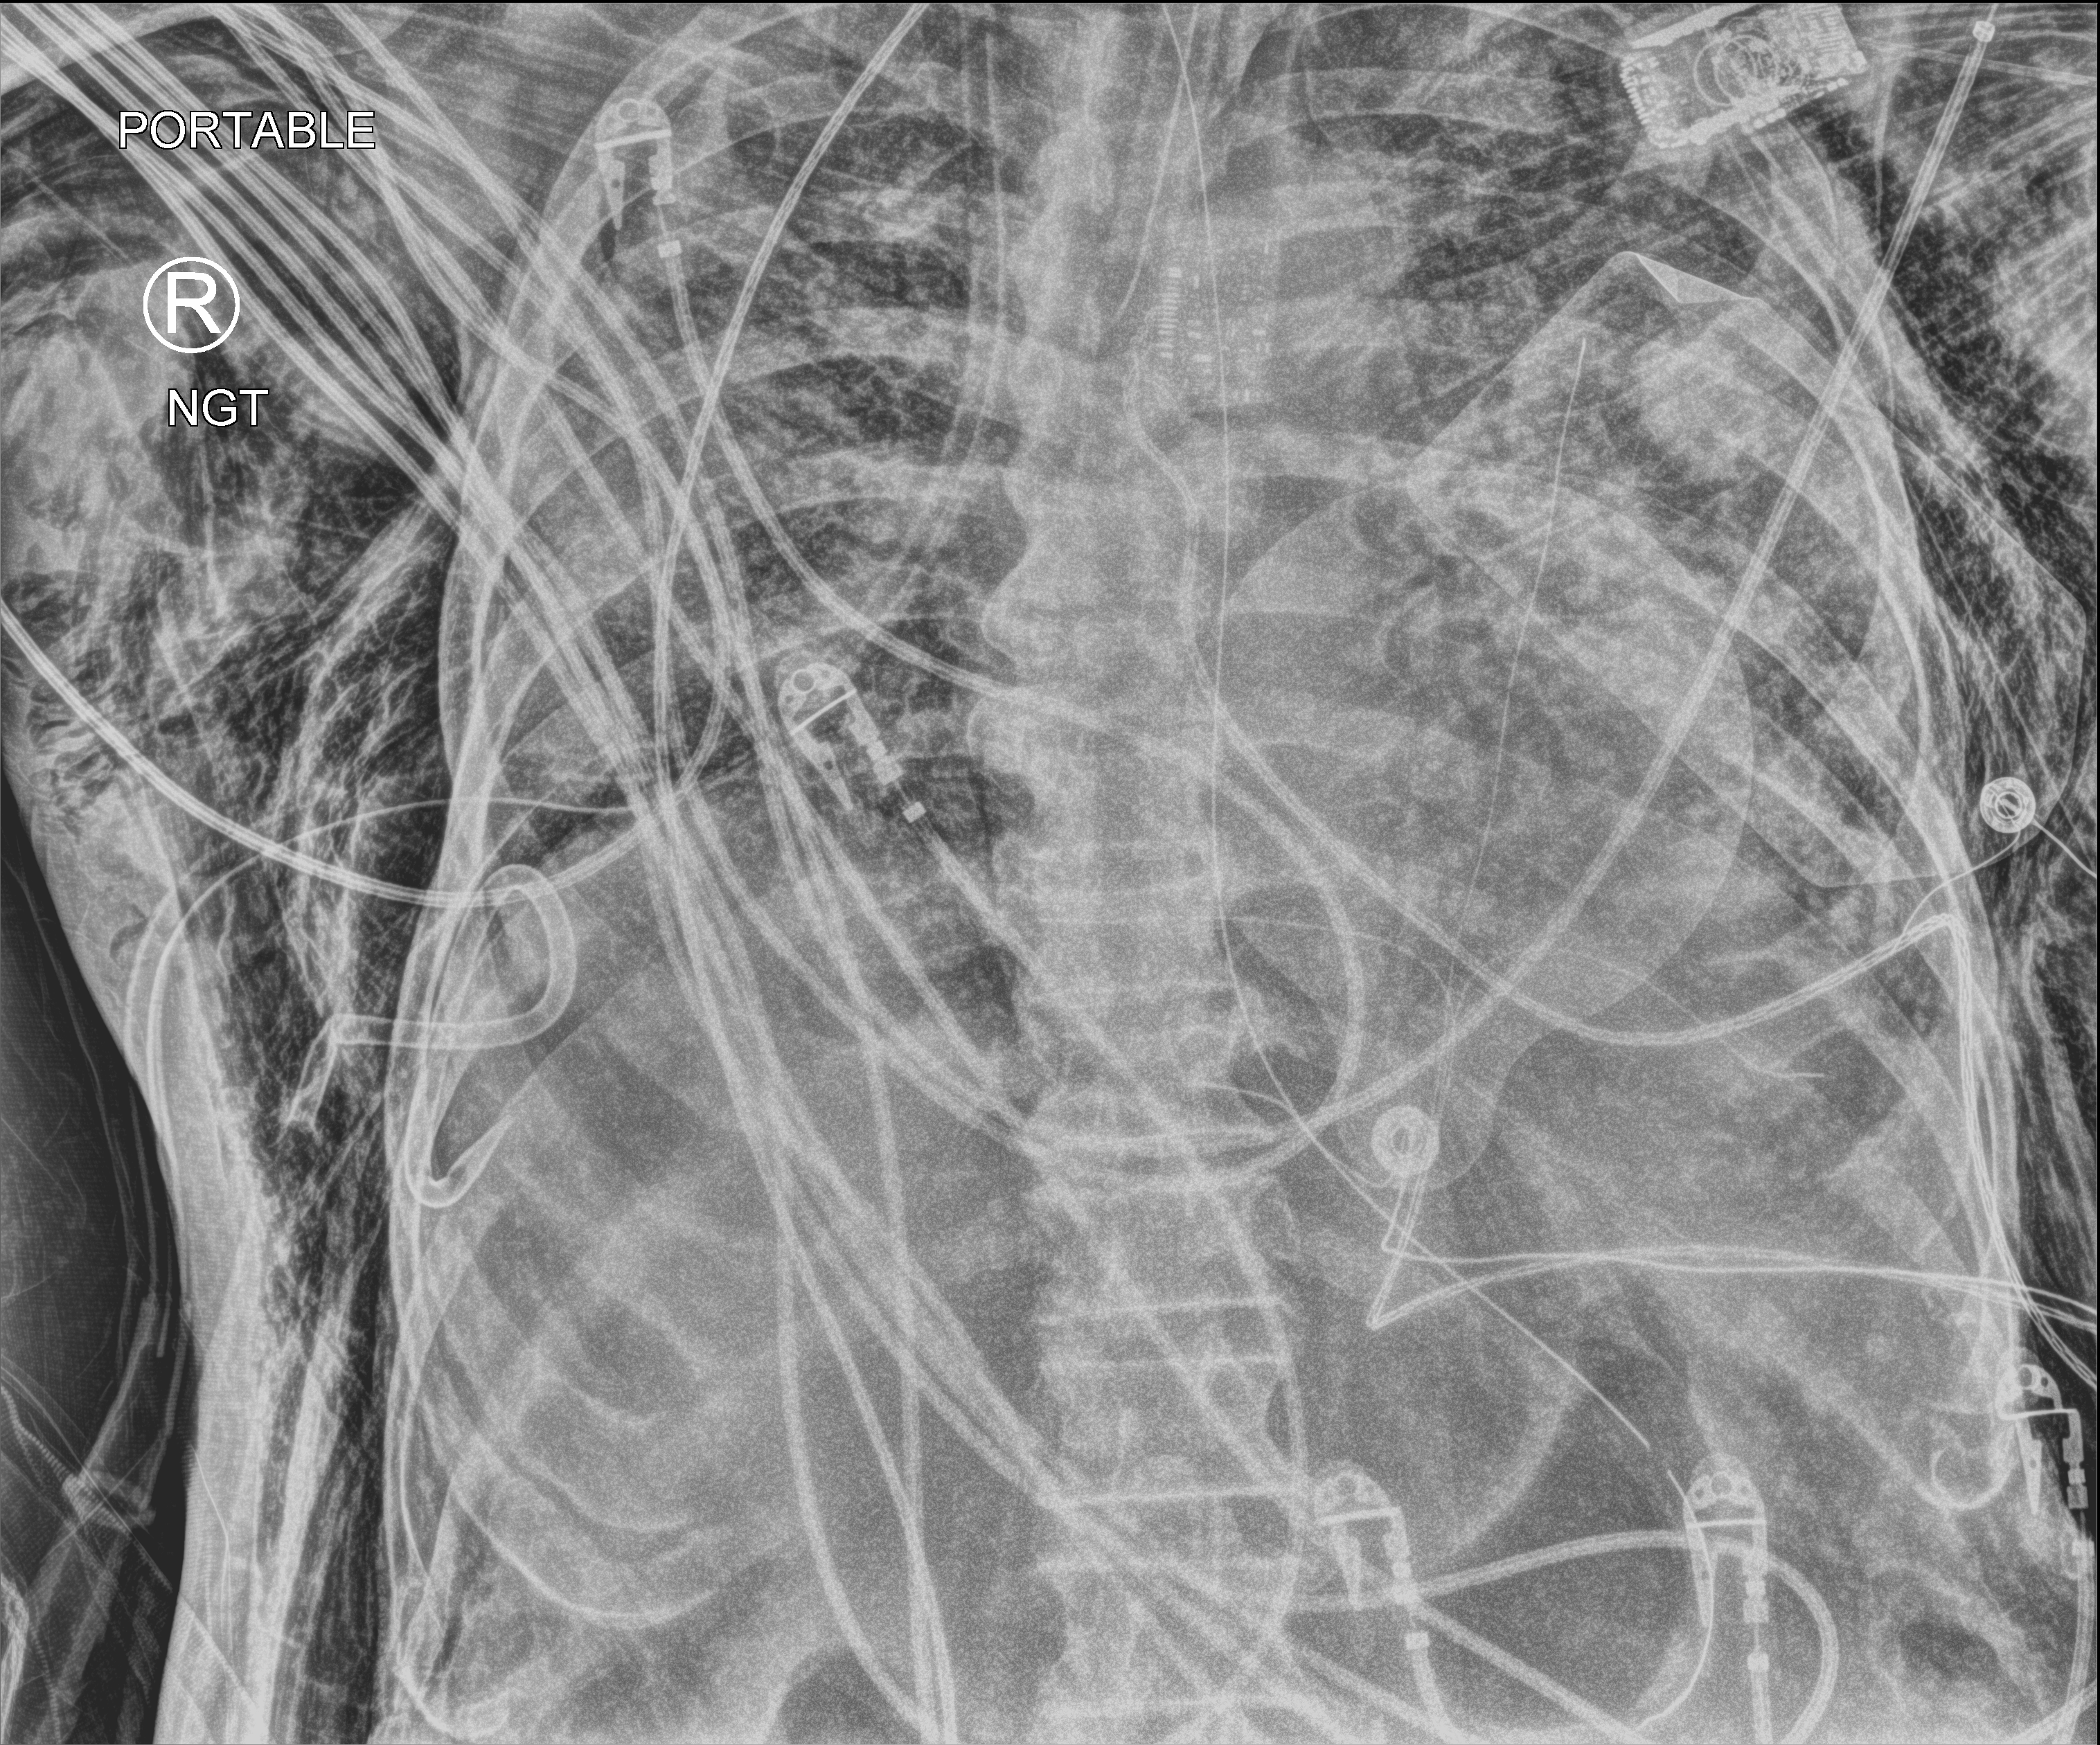
Portable chest radiograph. Patient hospitalised with COVID-19; male, aged 75–90 years.
Admission-level facts for this patient (not findings on this image; timing relative to this image not recorded): other chronic lung disease (admission record): no; admitted to intensive care during this hospital stay: yes; mechanically ventilated during this hospital stay: yes.